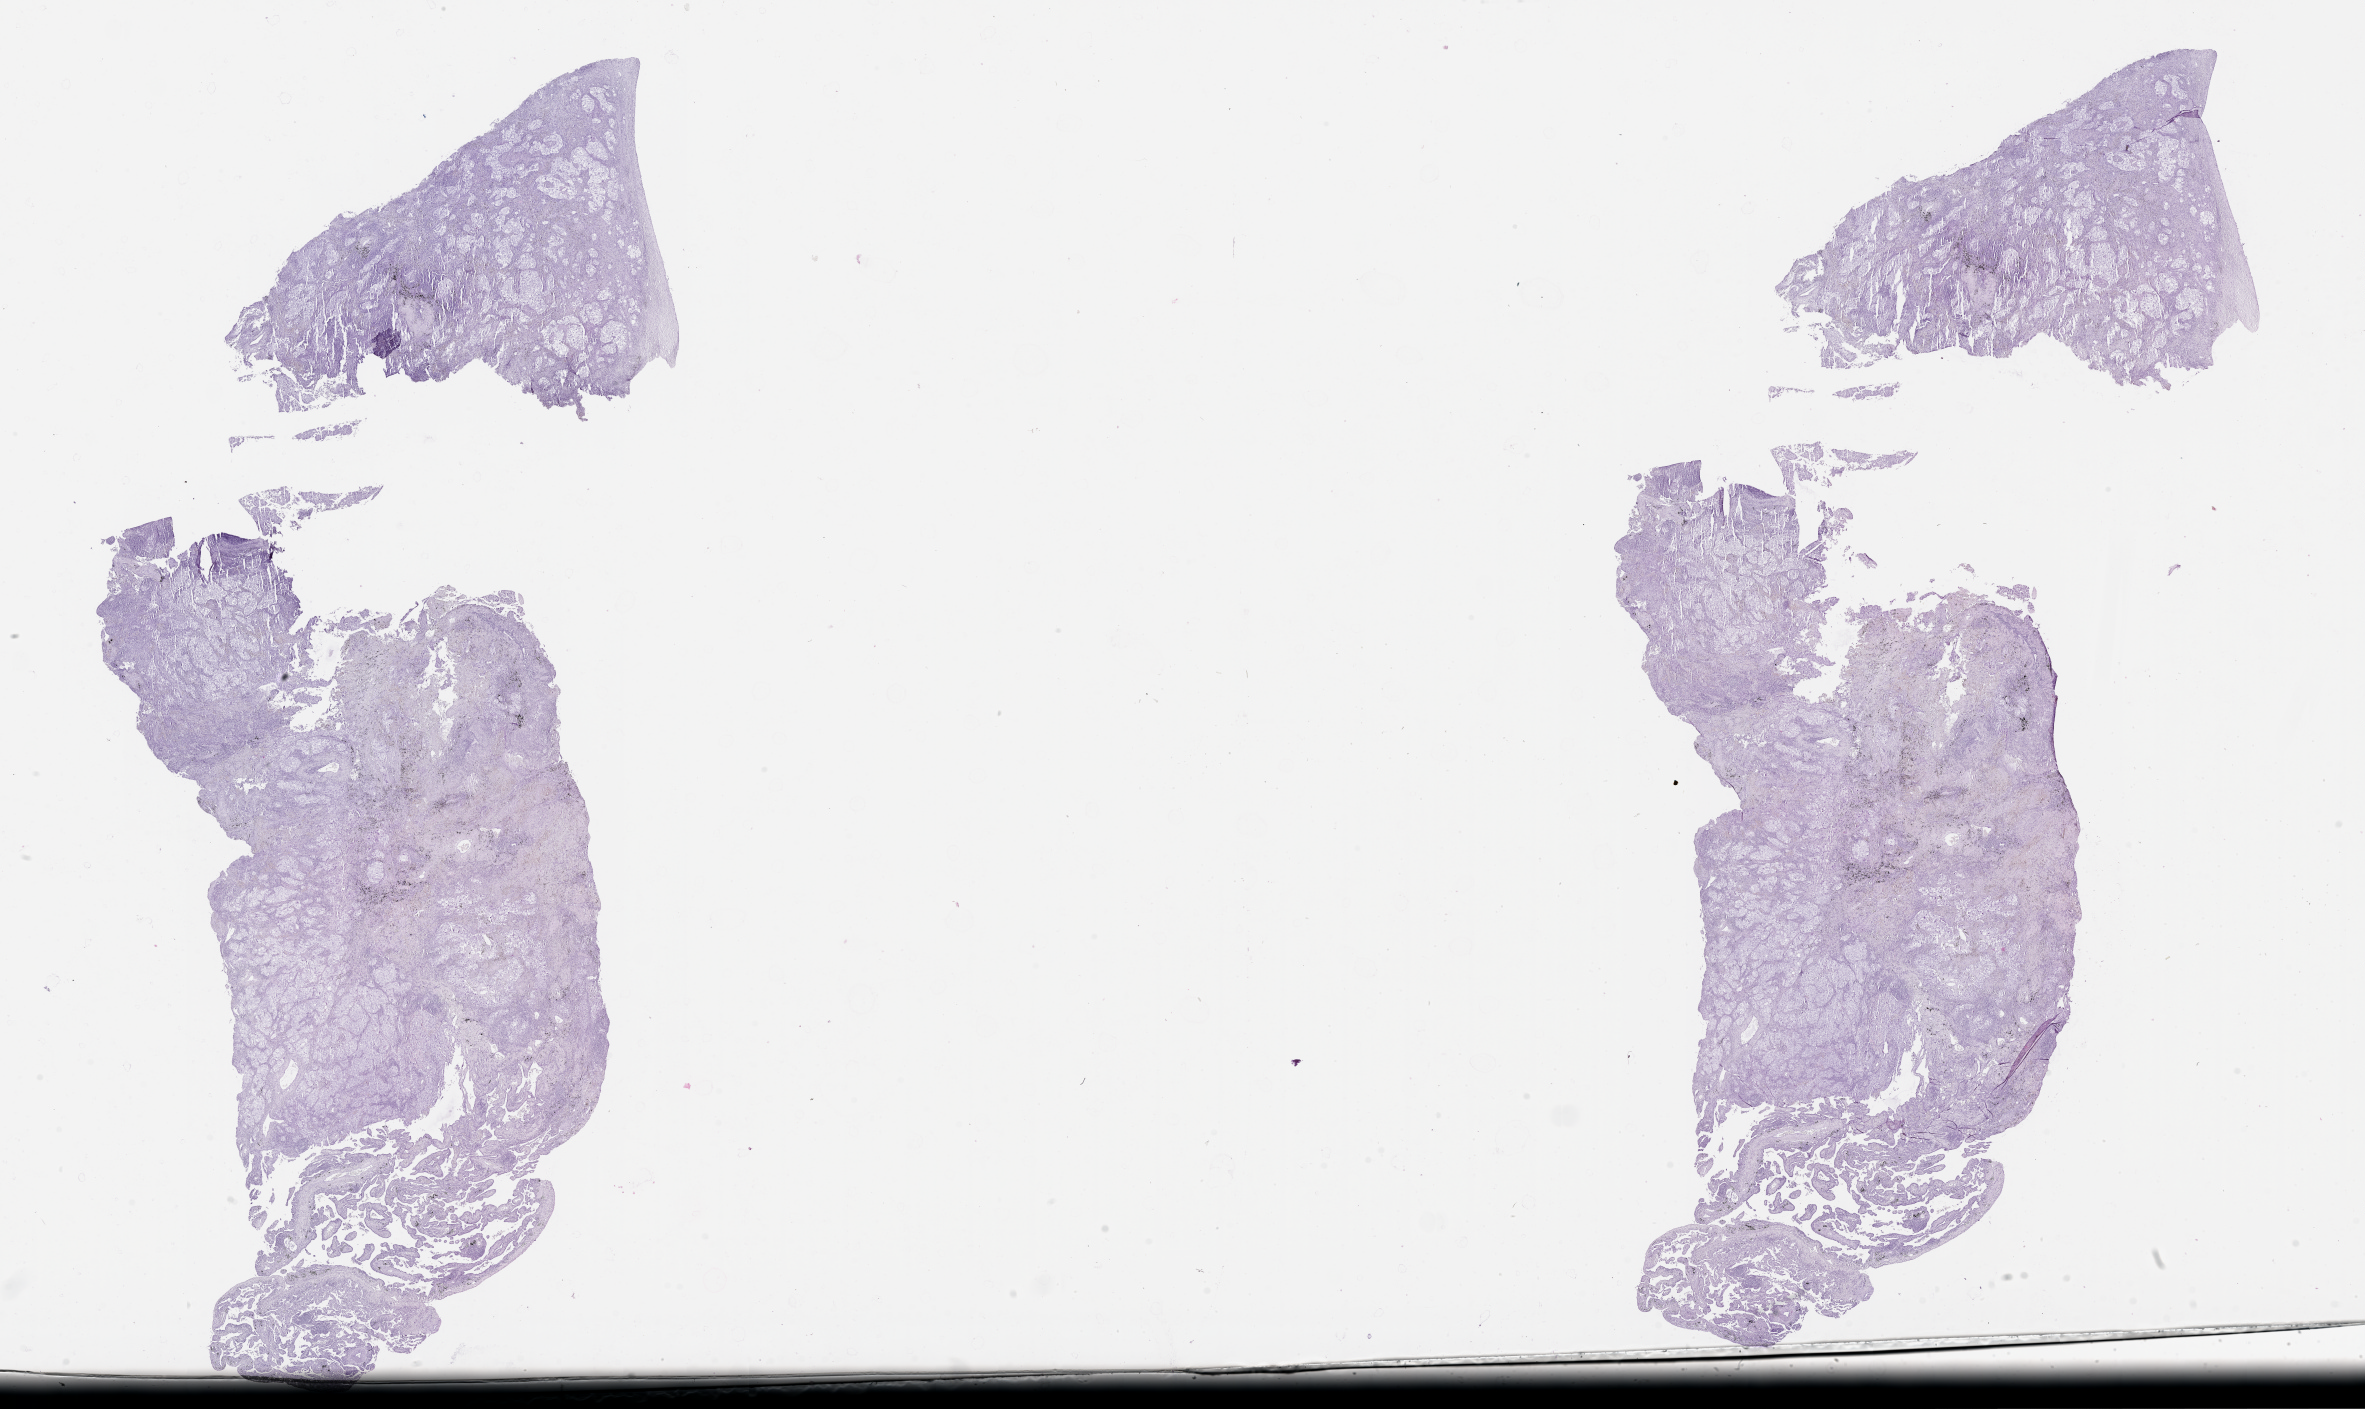
H&E whole-slide image, a low-resolution overview of the entire scanned area, about 38.1 x 22.7 mm (acquisition: 20x scan), tumour tissue sample, lung. 68-year-old male patient.
Patient diagnosis (cohort enrolment): squamous cell carcinoma (lung).